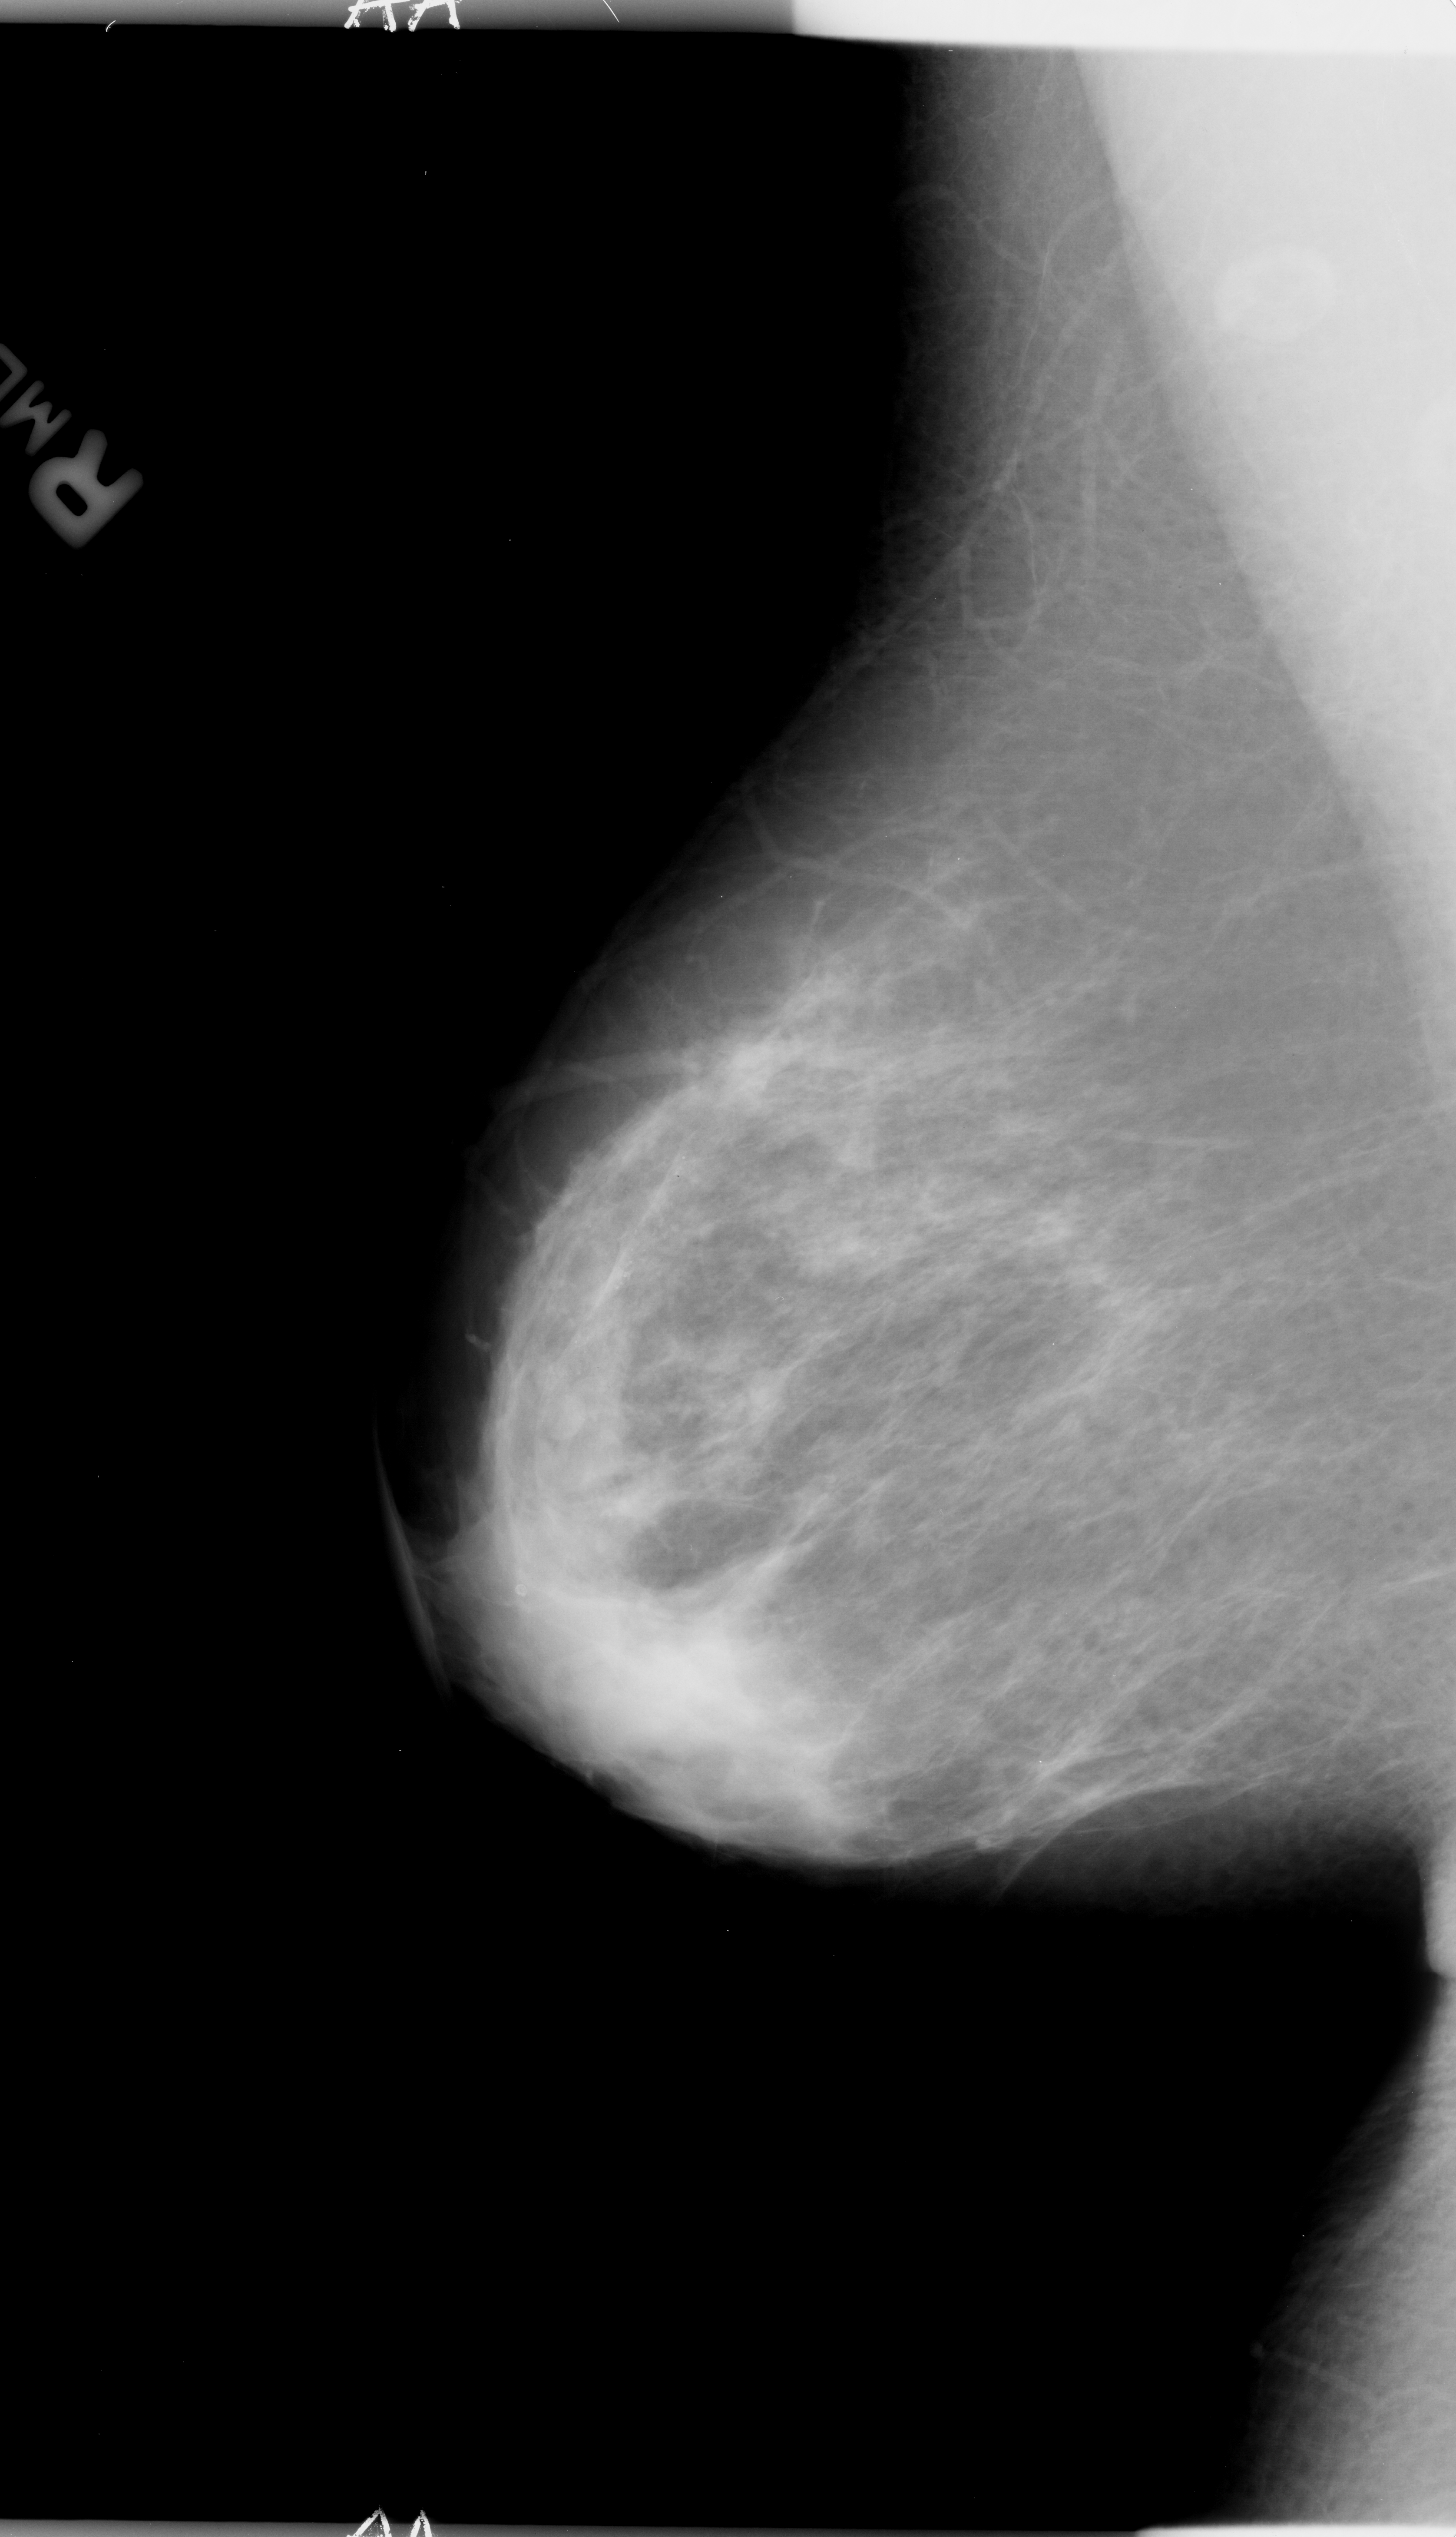
Scanned film-screen mammogram; right breast; mediolateral oblique (MLO) view; BI-RADS breast density category 3 (scale 1–4).
- Marked abnormality: calcifications, morphology pleomorphic, distribution segmental; BI-RADS assessment category 4; pathology result (as recorded, not read from the image): benign.